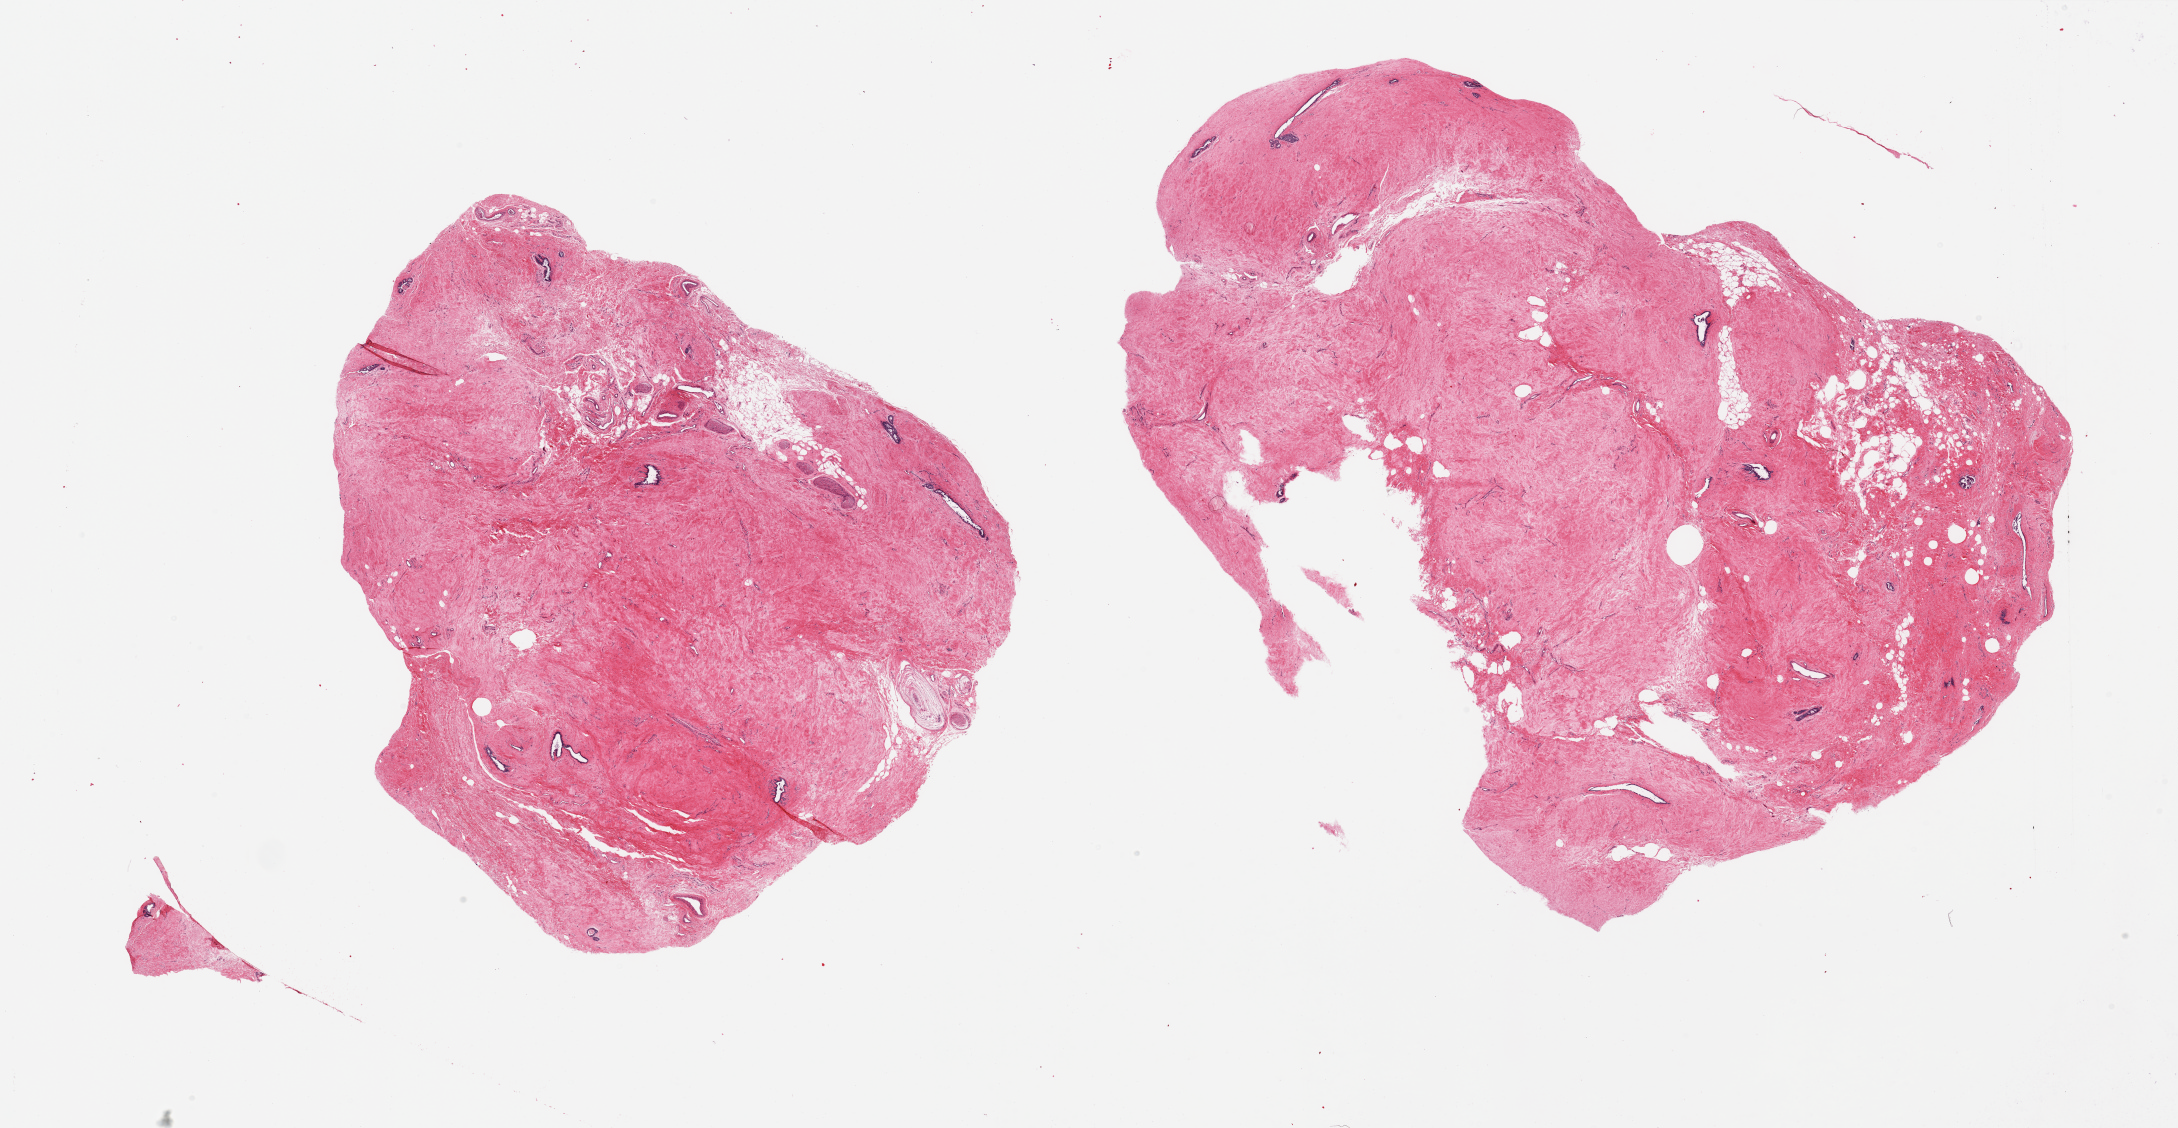
Digitized H&E-stained section — shown as a low-resolution overview of the whole scanned area (about 34.5 x 17.8 mm). PAXgene-fixed, paraffin-embedded tissue. Target tissue: breast. Tissue donor sample.
Reviewer comment on this tissue sample: 2 pieces; ducts and fibrous stroma with gynecomastoid changes.